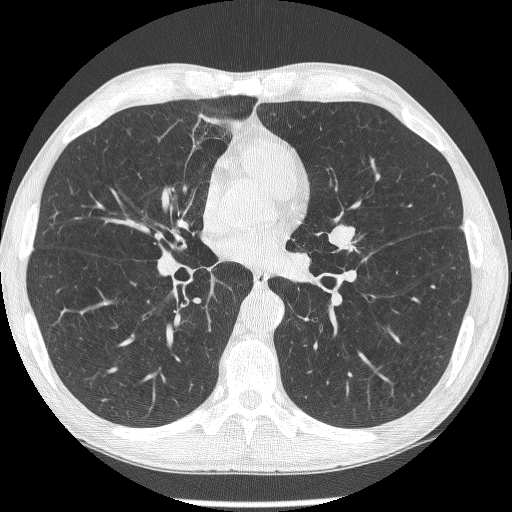
Axial slice from a low-dose chest CT screening exam; second screening round (one year after baseline); lung window (W 1500 / L -600 HU); 1.25 mm slice thickness; 120 kVp; slice 136 of 293 in the series. Male participant, aged 62 years at enrolment. Former smoker at enrolment.
Lesion marked by an expert reader, box from (x=320, y=217) to (x=369, y=265) px. The screening reader recorded 2 non-calcified nodules or masses ≥4 mm on this exam (lingula, lingula); which of them this box marks is not recorded.